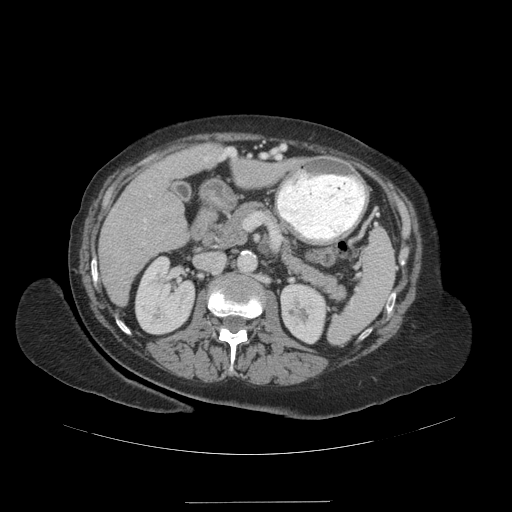
Contrast-enhanced abdominal CT (liver protocol), one axial slice; position 51 of 99 along the scan axis; reconstruction kernel STANDARD; soft-tissue window (W 400 / L 40 HU); 2.5 mm slice thickness; 512 × 512 image matrix, field of view 440 × 440 mm. From the clinical record (not read from this slice): diagnosis: hepatocellular carcinoma (patient treated with transarterial chemoembolisation; whether this scan precedes or follows treatment is not stated here); TNM stage (as recorded): Stage-IVA; Child-Pugh class: A; tumour nodularity: multinodular.
Outlined on this slice (semi-automatically segmented with operator editing):
- liver parenchyma outside the tumour (the mass and vessels are separate outlines, so this box may not span the whole liver): bounding box (x1, y1, x2, y2) in pixels: (98, 144, 286, 304)
- liver vessels: (144, 148, 236, 222)